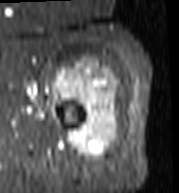
MRI of an extremity soft-tissue mass, one axial slice; position 85 of 103 along the scan axis; STIR; MR volume resampled by the dataset authors to the PET/CT grid (not the native acquisition matrix); 179 × 193 image matrix, field of view 175 × 188 mm. Female patient. From the clinical record (not read from this slice): histological type: undifferentiated – high grade; grade: high; site of the primary tumour: left thigh.
Outlined on this slice (expert contour drawn on MRI and transferred to this co-registered scan by the dataset authors):
- gross tumour volume including surrounding oedema: bounding box (x1, y1, x2, y2) in pixels: (52, 58, 119, 163)
- gross tumour volume (mass): (54, 62, 119, 163)